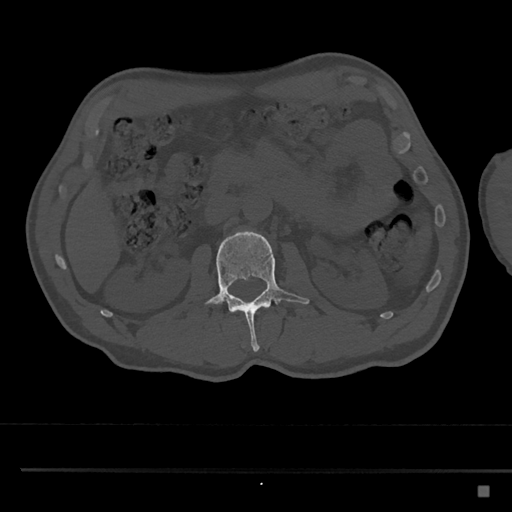
CT including the spine, one axial slice. Position 760 of 797 along the scan axis. Reconstruction kernel Br40s/3. Bone window (W 1800 / L 400 HU). 0.5 mm slice thickness. 512 × 512 image matrix, field of view 391 × 391 mm. Patient: male, 59 years. From the clinical record (not read from this slice): primary cancer: prostate.
Outlined on this slice (semi-automatically segmented with operator editing):
- L2 vertebra: bounding box (x1, y1, x2, y2) in pixels: (206, 230, 310, 352)